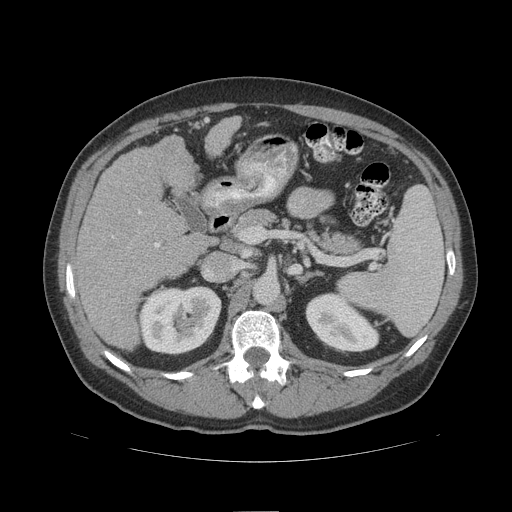
Contrast-enhanced abdominal CT (liver protocol), one axial slice. Slice 57 of 109 in the series (ordered by position). Soft-tissue window (W 400 / L 40 HU). 2.5 mm slice thickness. 512 × 512 image matrix, field of view 420 × 420 mm. Case-level facts recorded for this patient, not image findings: diagnosis: hepatocellular carcinoma (patient treated with transarterial chemoembolisation; whether this scan precedes or follows treatment is not stated here); TNM stage (as recorded): Stage-IIIB; Child-Pugh class: A.
Annotated regions visible in this slice (semi-automatic segmentation, software-assisted and operator-edited):
- liver parenchyma outside the tumour (the mass and vessels are separate outlines, so this box may not span the whole liver): bounding box (x1, y1, x2, y2) in pixels: (76, 116, 240, 350)
- liver vessels: (138, 210, 160, 247)